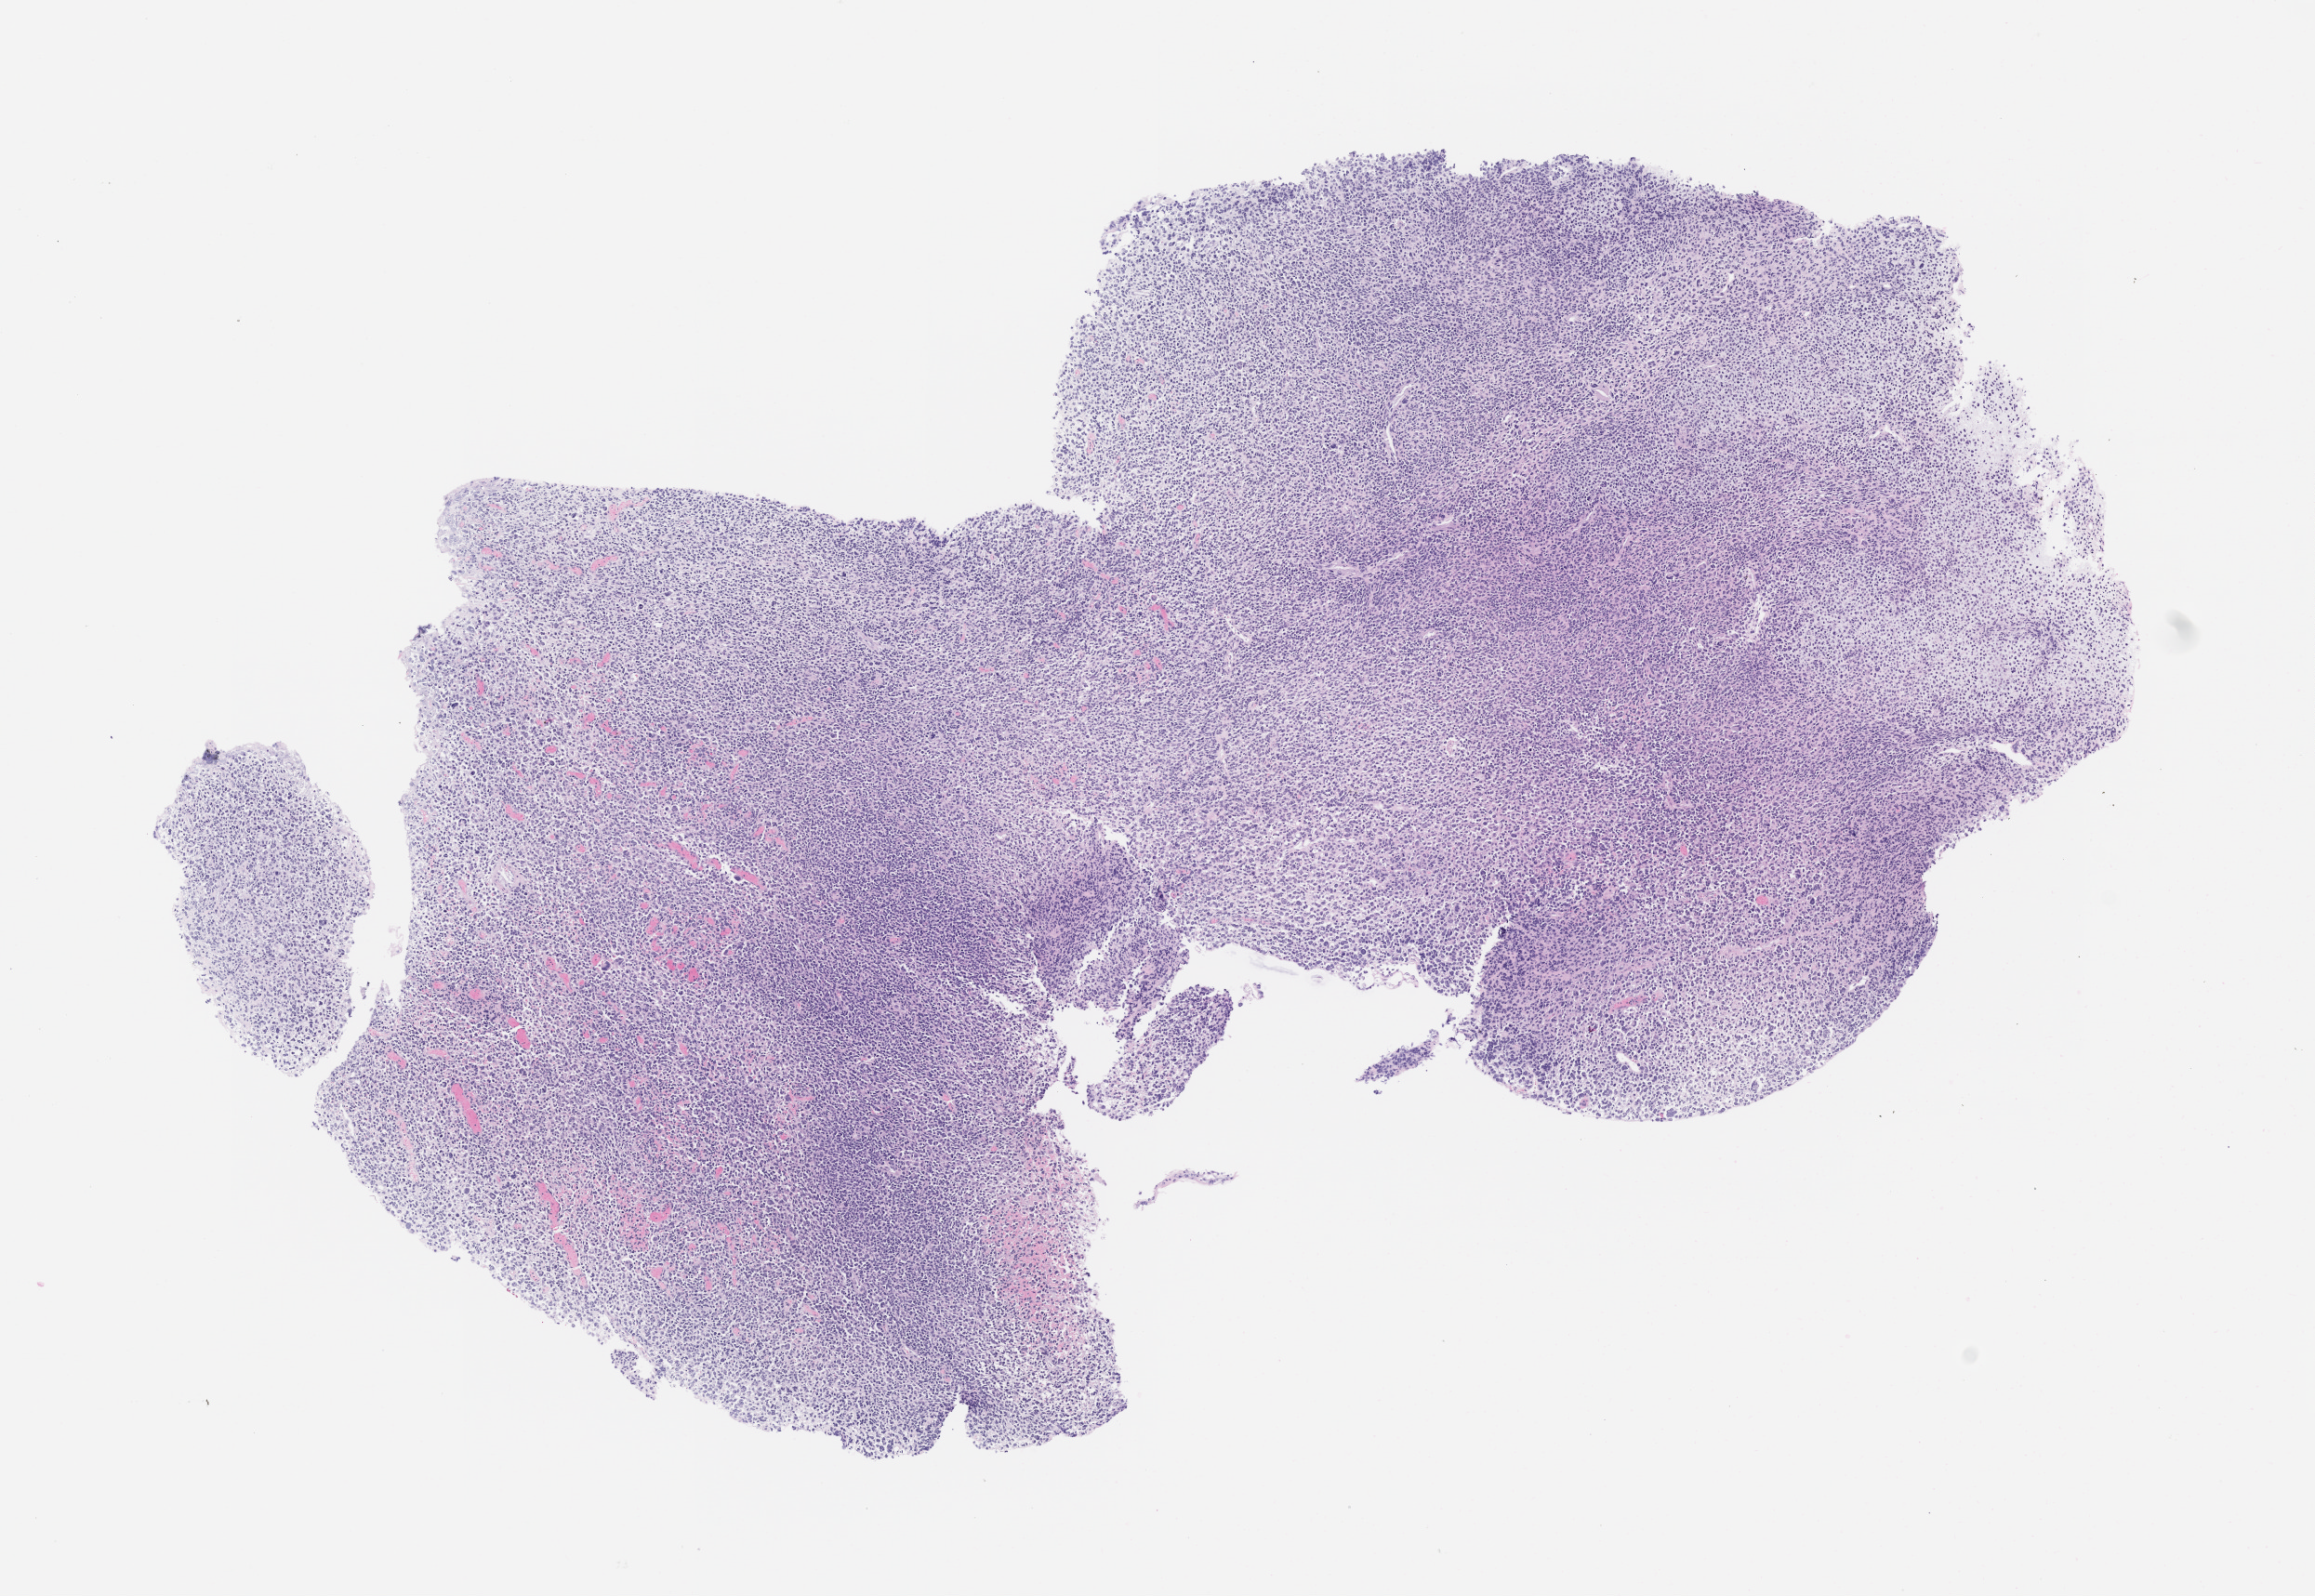
Whole-slide image, haematoxylin and eosin stain of the patient's (originator) tumor tissue — whole scanned area (about 10.0 x 6.9 mm) shown as a low-resolution overview; FFPE section; tumor site category: bladder. Patient male; 76 years old.
- diagnosis: Urothelial Carcinoma